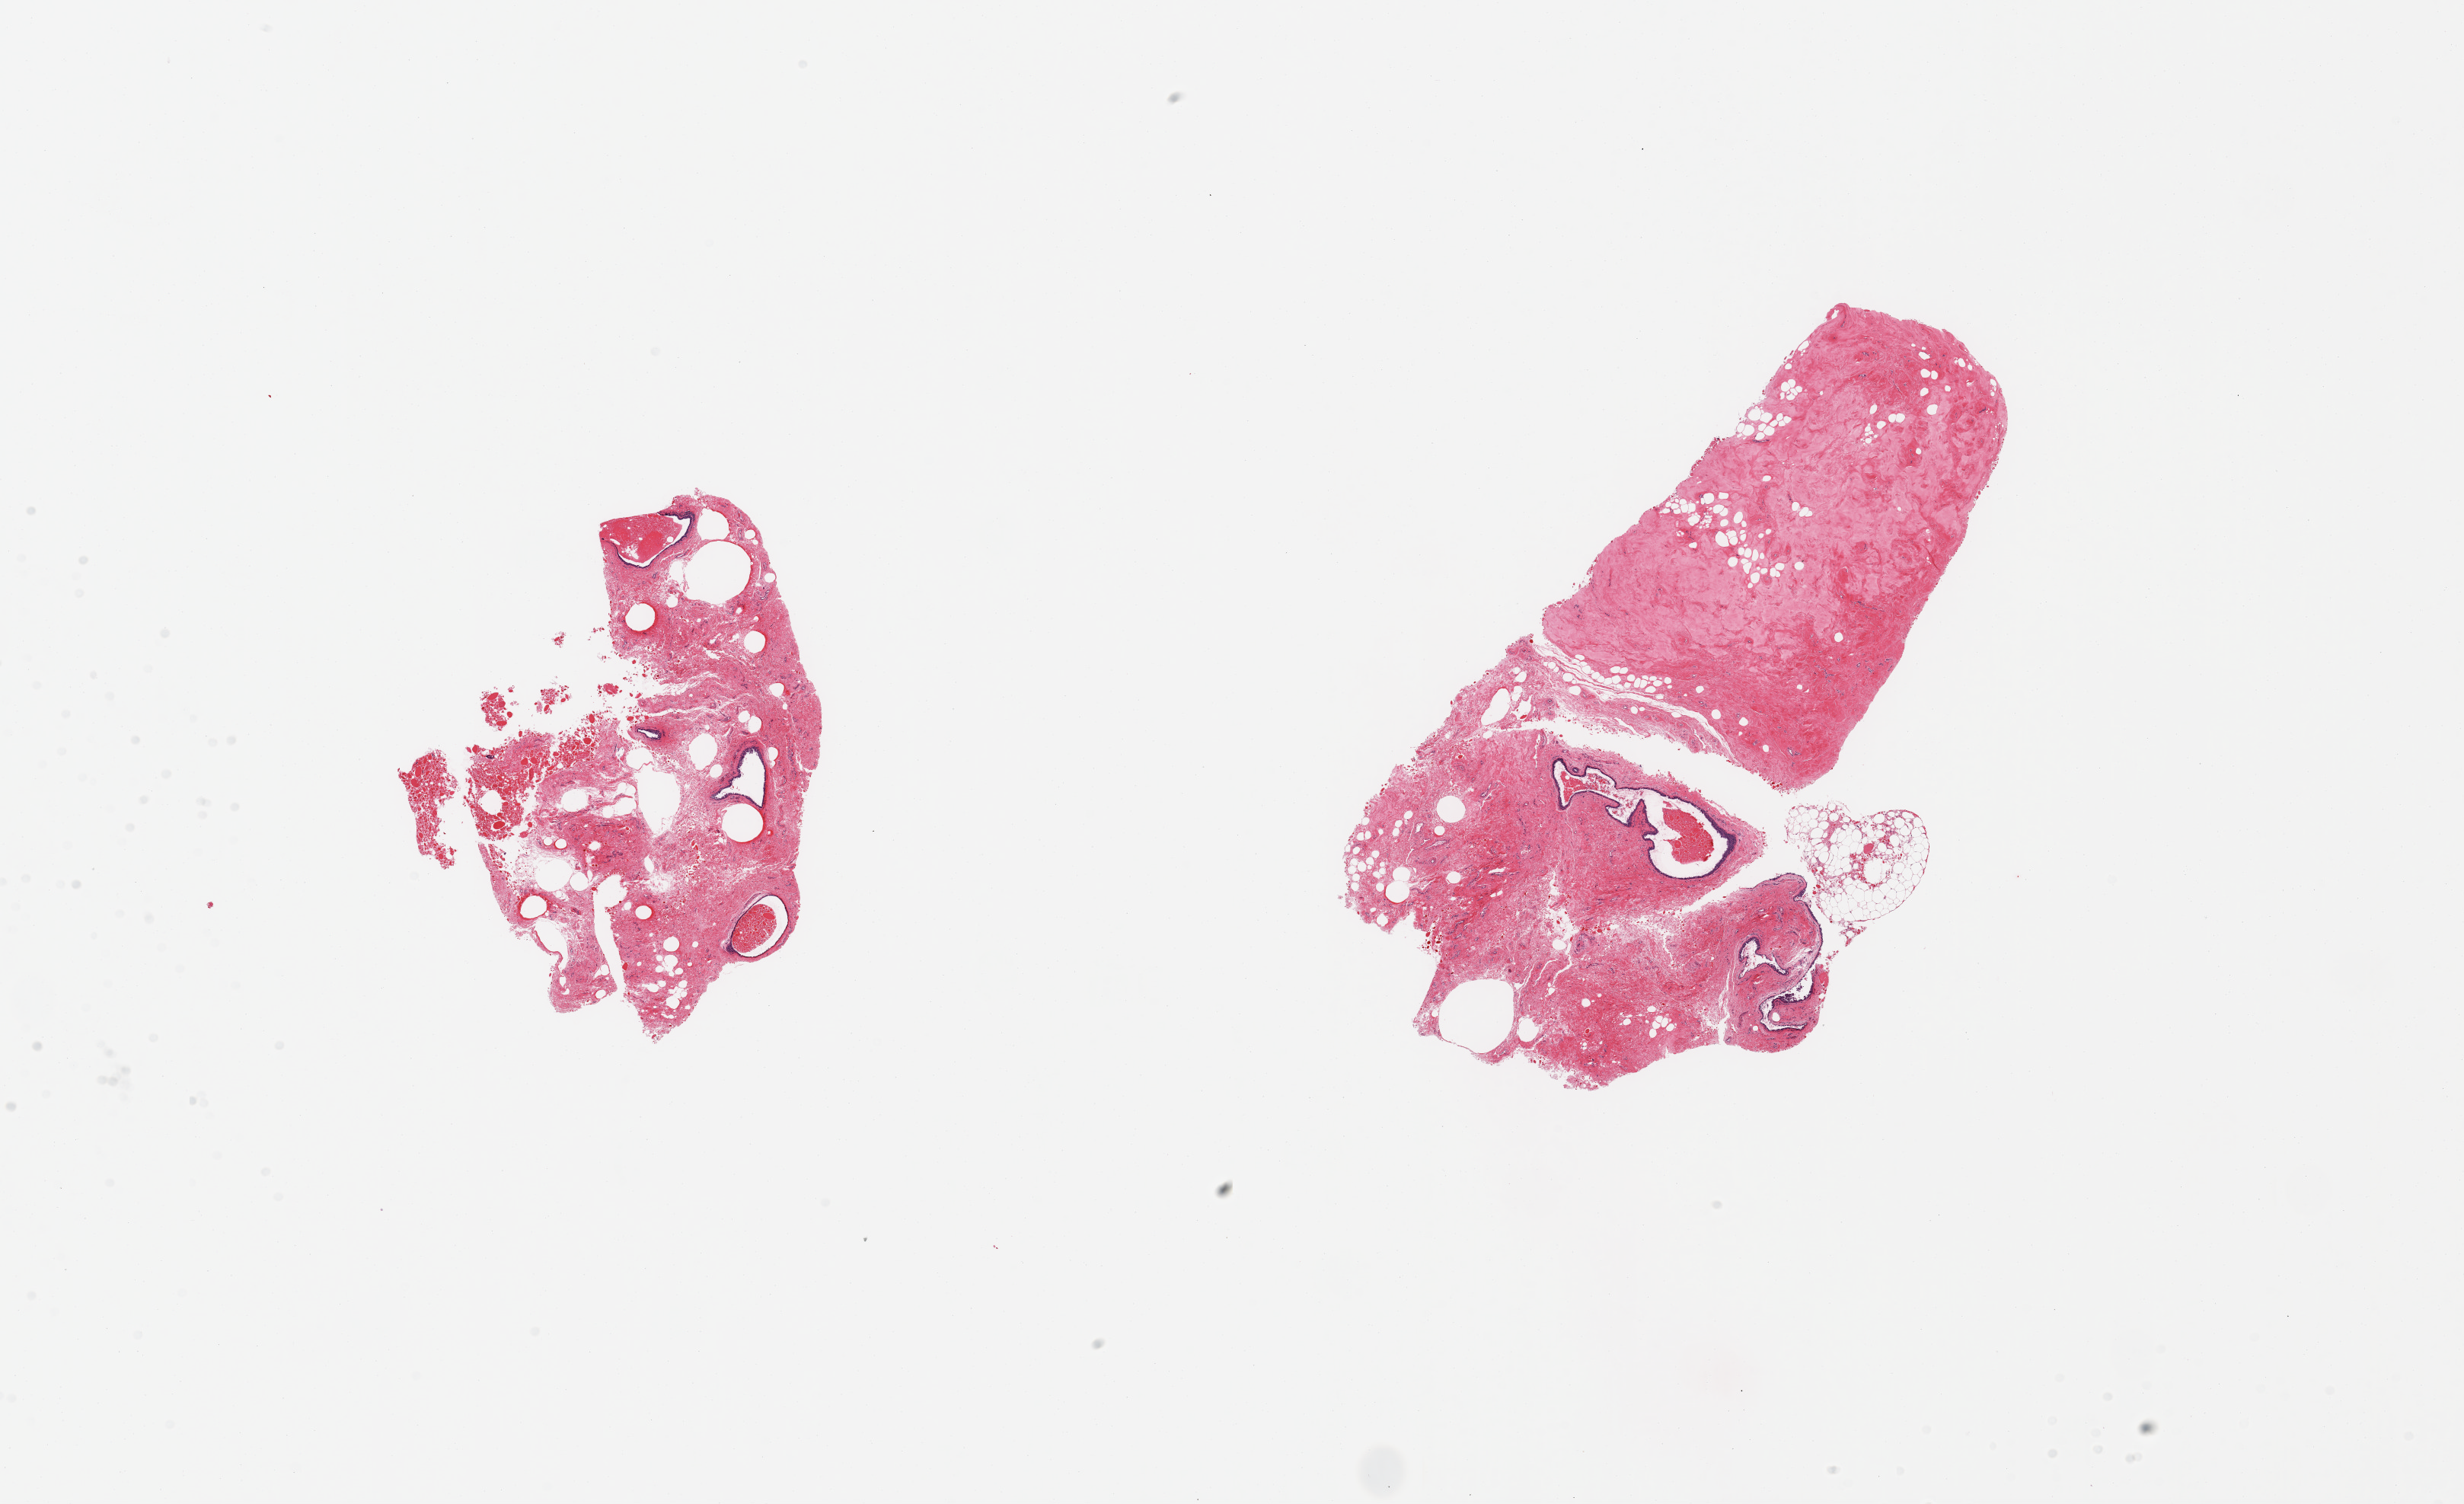
Digitized hematoxylin and eosin (H&E)-stained section — shown as a low-resolution overview of the whole scanned area (about 25.6 x 15.6 mm, acquisition: 20x scan). PAXgene-fixed, paraffin-embedded tissue. Target tissue: breast. Tissue donor sample. Donor sex: female.
Pathologist's review note for this sample: 2 pieces; atrophic cystic ducts and dense fibrous tissue; 1 piece has 20% skeletal muscle content.